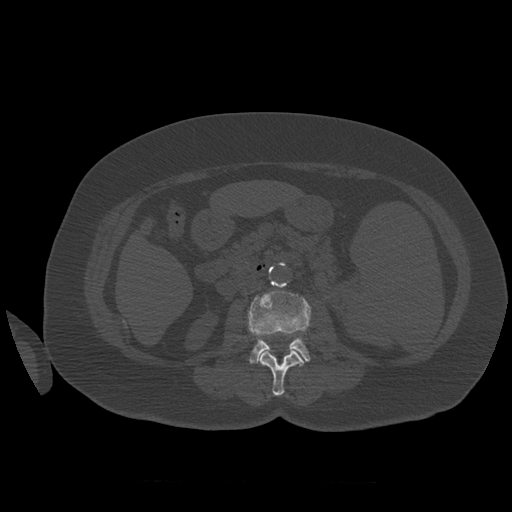
CT including the spine, one axial slice; slice 241 of 399 in the series (ordered by position); reconstruction kernel STANDARD; bone window (W 1800 / L 400 HU); 1.25 mm slice thickness; 512 × 512 image matrix, field of view 404 × 404 mm. Patient age 81 years. From the clinical record (not read from this slice): primary cancer: renal.
Outlined on this slice (semi-automatically segmented with operator editing):
- L2 vertebra: bounding box (x1, y1, x2, y2) in pixels: (260, 347, 305, 396)
- L3 vertebra: (248, 289, 311, 364)